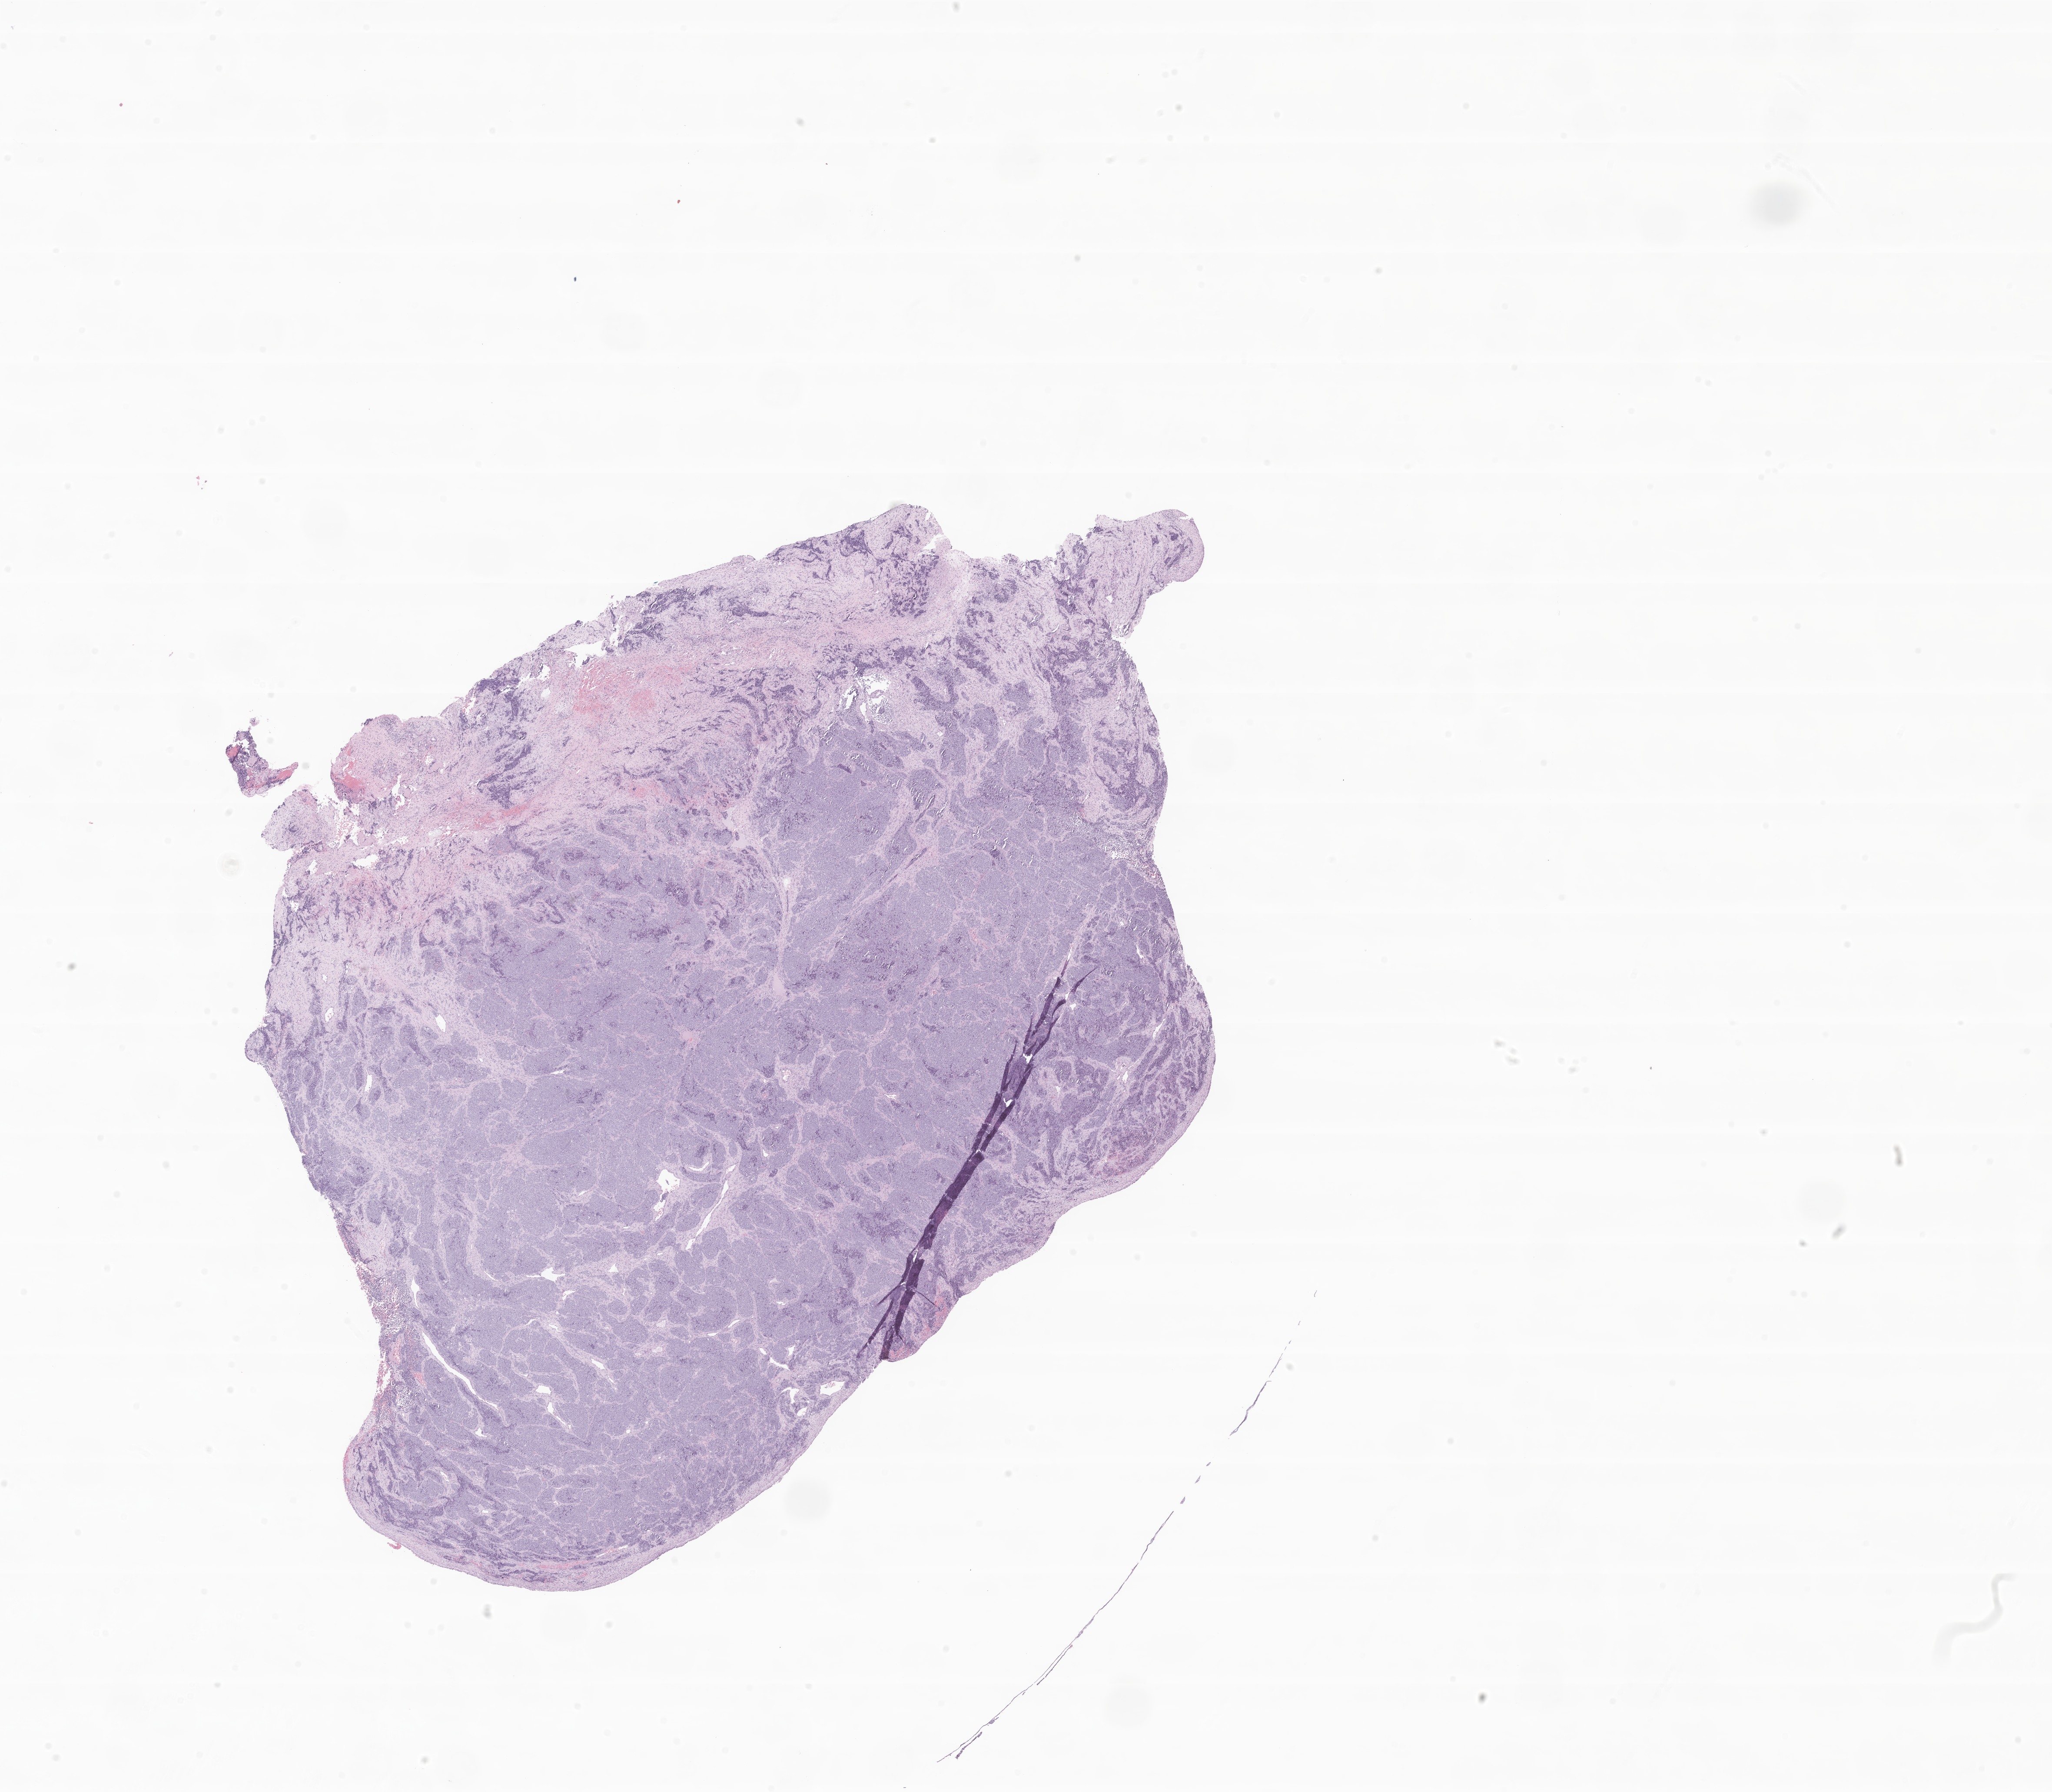
Digitized hematoxylin and eosin (H&E)-stained section of tumor tissue from the nasopharynx — whole scanned area (about 19.9 x 17.4 mm) shown as a low-resolution overview, formalin-fixed paraffin-embedded section. Patient: female, age 177 months (14 years 9 months).
* diagnosis (ICD-O-3 morphology term): Rhabdomyosarcoma, NOS